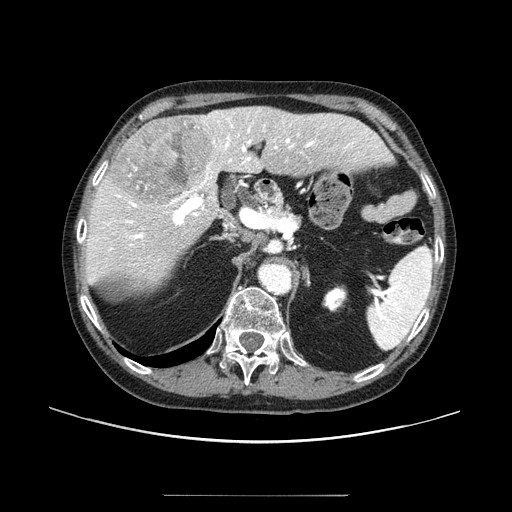
Contrast-enhanced abdominal CT (liver protocol), one axial slice. Slice 55 of 91 in the series (ordered by position). 100 kVp. One of 2 acquisitions stored at this slice position. Soft-tissue window (W 400 / L 40 HU). 2.5 mm slice thickness. 512 × 512 image matrix, field of view 400 × 400 mm. Case-level facts recorded for this patient, not image findings: diagnosis: hepatocellular carcinoma (patient treated with transarterial chemoembolisation; whether this scan precedes or follows treatment is not stated here); TNM stage (as recorded): Stage-I; Child-Pugh class: A; tumour differentiation: moderately differentiated; tumour nodularity: uninodular.
Annotated regions visible in this slice (semi-automatic segmentation, software-assisted and operator-edited):
- liver parenchyma outside the tumour (the mass and vessels are separate outlines, so this box may not span the whole liver): box from (x=86, y=106) to (x=356, y=284) px
- mass: (x=111, y=116)–(x=215, y=210)
- liver vessels: (x=104, y=111)–(x=323, y=251)